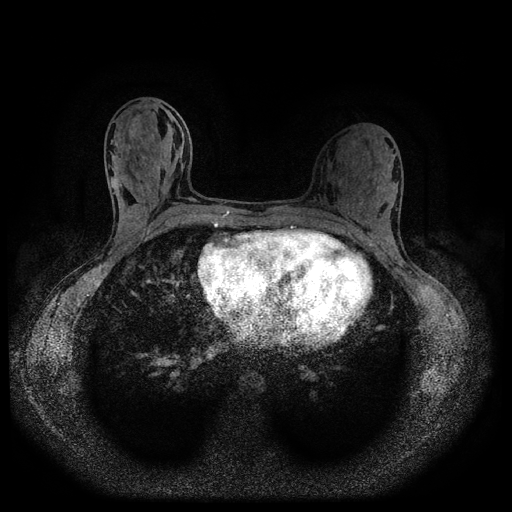
Breast MRI (dynamic contrast-enhanced, multi-phase), one axial slice. Slice 46 of 116 in the series (ordered by position). Dynamic contrast-enhanced series, time point 2 of 5 at this slice position (early post-contrast). 1.5 T. TE 2.7 ms, TR 5.4 ms. 512 × 512 image matrix, field of view 330 × 330 mm. Patient: female, 32 years.
Annotated regions visible in this slice (semi-automatic segmentation, software-assisted and operator-edited):
- breast lesion (labelled benign in the annotation): bounding box [x1, y1, x2, y2] px = [127, 115, 142, 139]